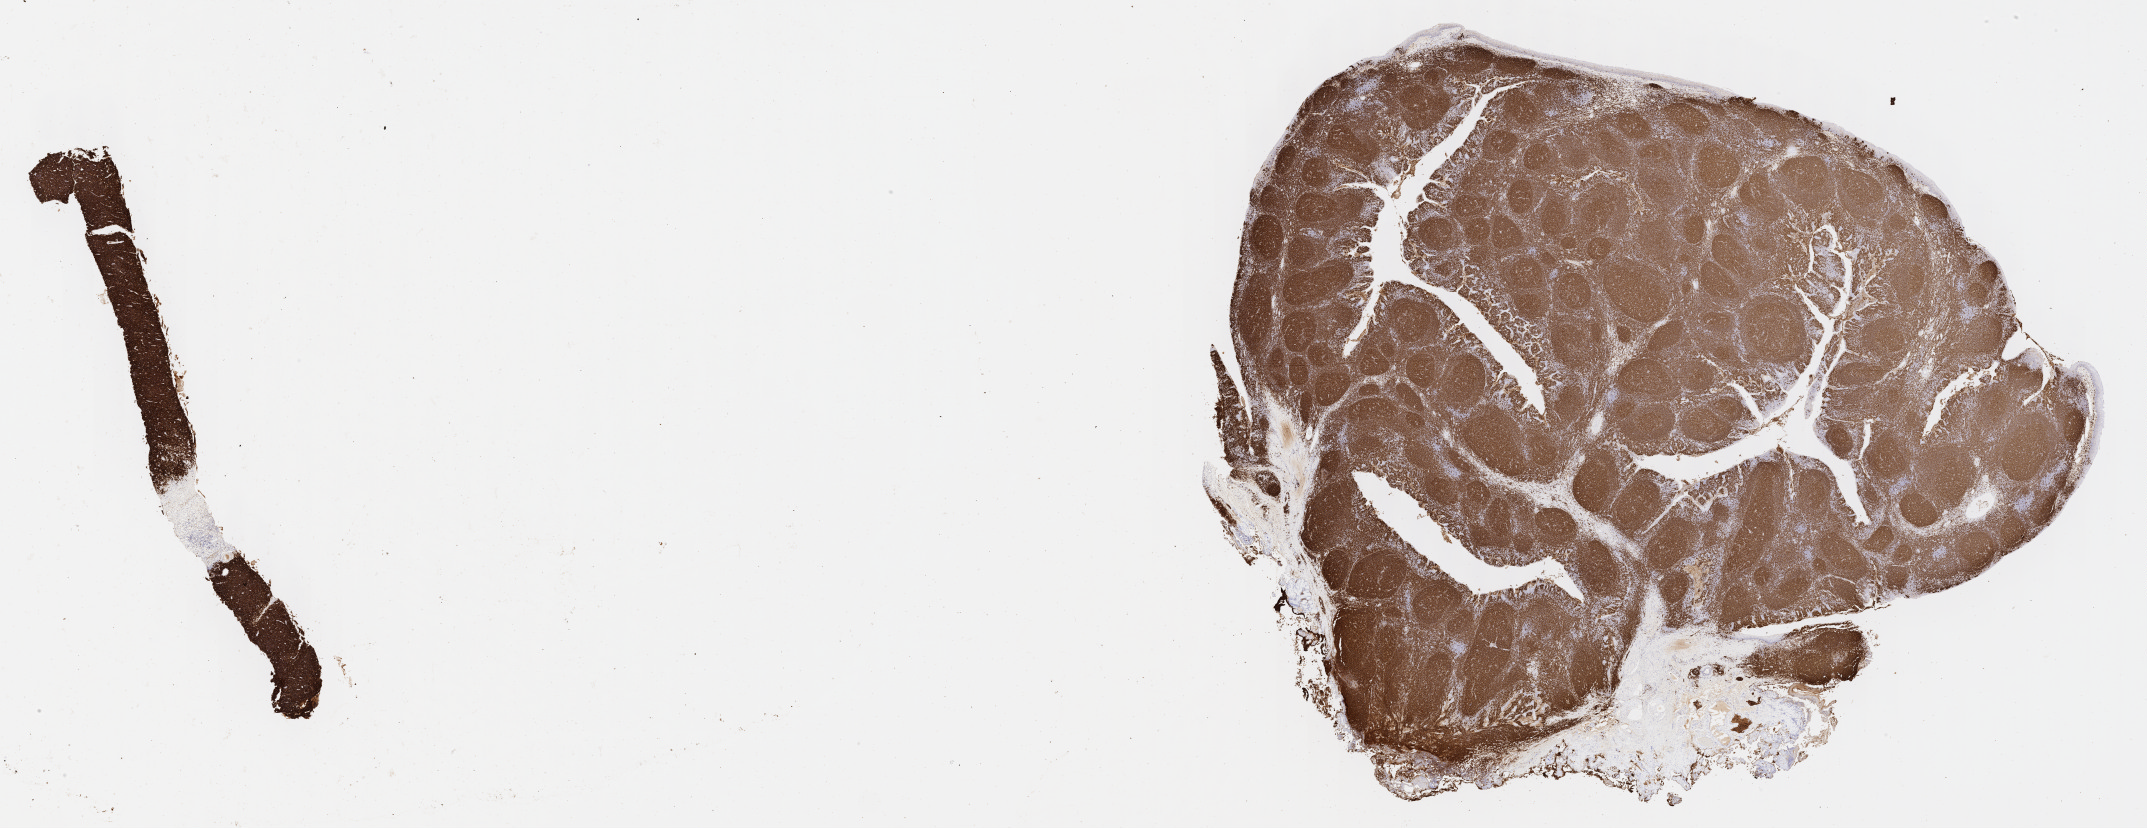
Immunohistochemistry (IHC) whole-slide image stained for CD20 — shown as a low-resolution overview of the whole scanned area (about 34.7 x 13.4 mm), tumor tissue. Patient: male, age at initial diagnosis 7 years.
Histologic diagnosis: Neoplasm, uncertain whether benign or malignant.